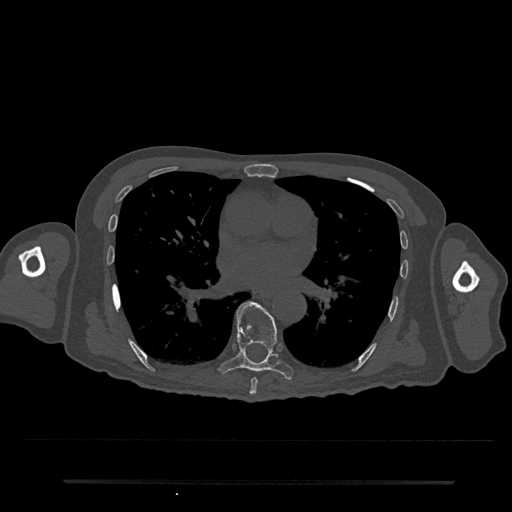
CT including the spine, one axial slice; position 433 of 797 along the scan axis; reconstruction kernel Br40s/3; bone window (W 1800 / L 400 HU); 0.5 mm slice thickness; 512 × 512 image matrix, field of view 427 × 427 mm. Male patient, age 74 years. From the clinical record (not read from this slice): primary cancer: prostate.
Structures marked on this image (semi-automatic segmentation, software-assisted and operator-edited):
- T7 vertebra: bounding box (x1, y1, x2, y2) in pixels: (249, 378, 258, 395)
- T8 vertebra: (218, 301, 294, 380)